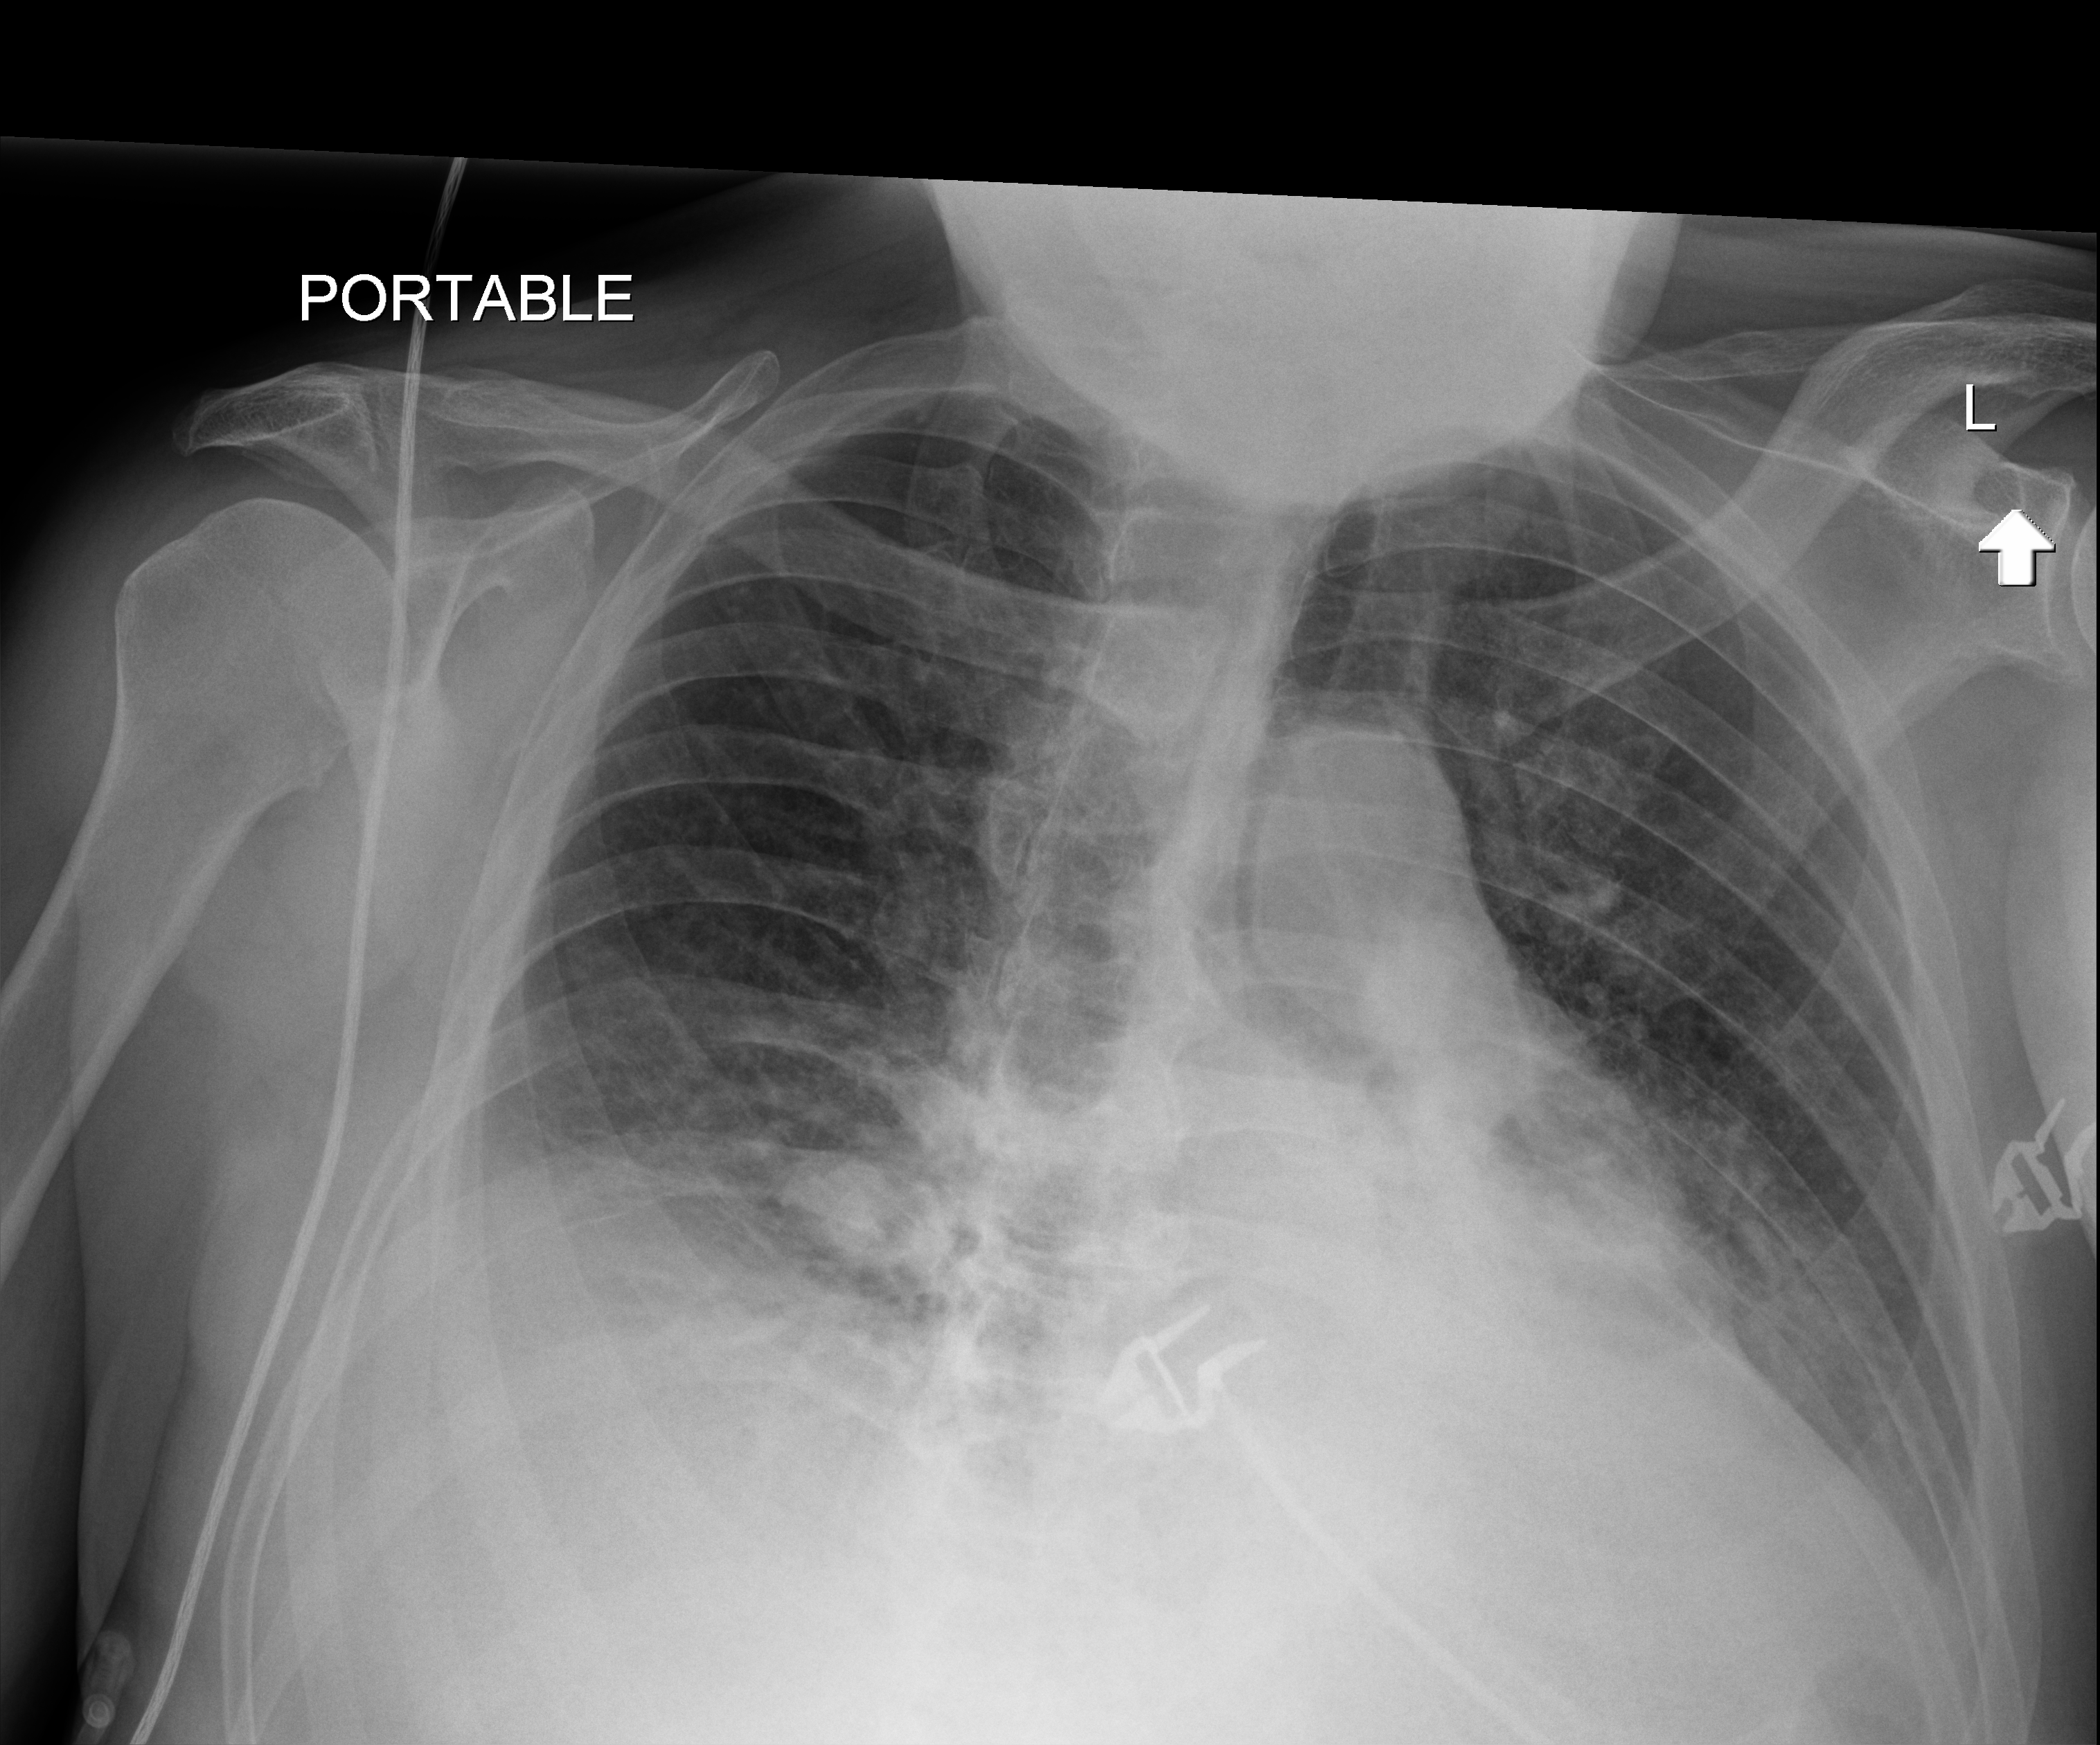
Chest radiograph (digital radiography); anteroposterior (AP) projection. Male patient hospitalised with COVID-19, age 18–59 years.
Hospital-stay facts (about this admission, not read from this image; timing relative to this image not recorded): mechanically ventilated during this hospital stay: no.